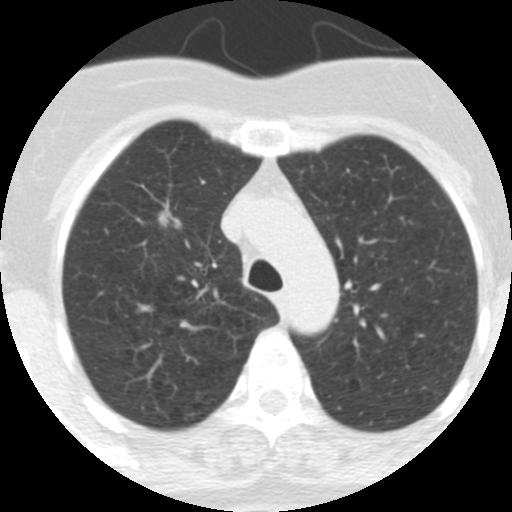
Chest CT (low-dose screening protocol), one axial image, first (baseline) screen, lung window (W 1500 / L -600 HU), 2.5 mm slice thickness, slice 77 of 313 in the series. Female participant, aged 62 years at enrolment. Current smoker at enrolment.
- Expert-annotated lung lesion, bounding box (x1, y1, x2, y2) in pixels: (116, 158, 182, 232).
- The exam's reader record, not a measurement of the box and not confirmed to be the same lesion: non-calcified nodule or mass ≥4 mm, right upper lobe, 9 × 7 mm, spiculated (stellate) margins, soft tissue attenuation.